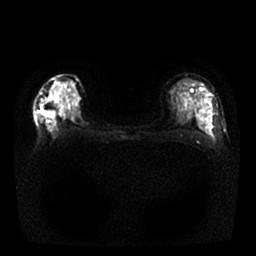
Breast MRI, one axial slice; slice 12 of 25 in the series (ordered by position); diffusion-weighted series; image 2 of 4 stored at this slice position (different b-values; order by instance number); 1.5 T; 4 mm slice thickness; 256 × 256 image matrix, field of view 330 × 330 mm. Female patient.
Structures marked on this image (expert manual segmentation):
- tumour on diffusion-weighted imaging: bounding box [x1, y1, x2, y2] px = [43, 111, 54, 118]